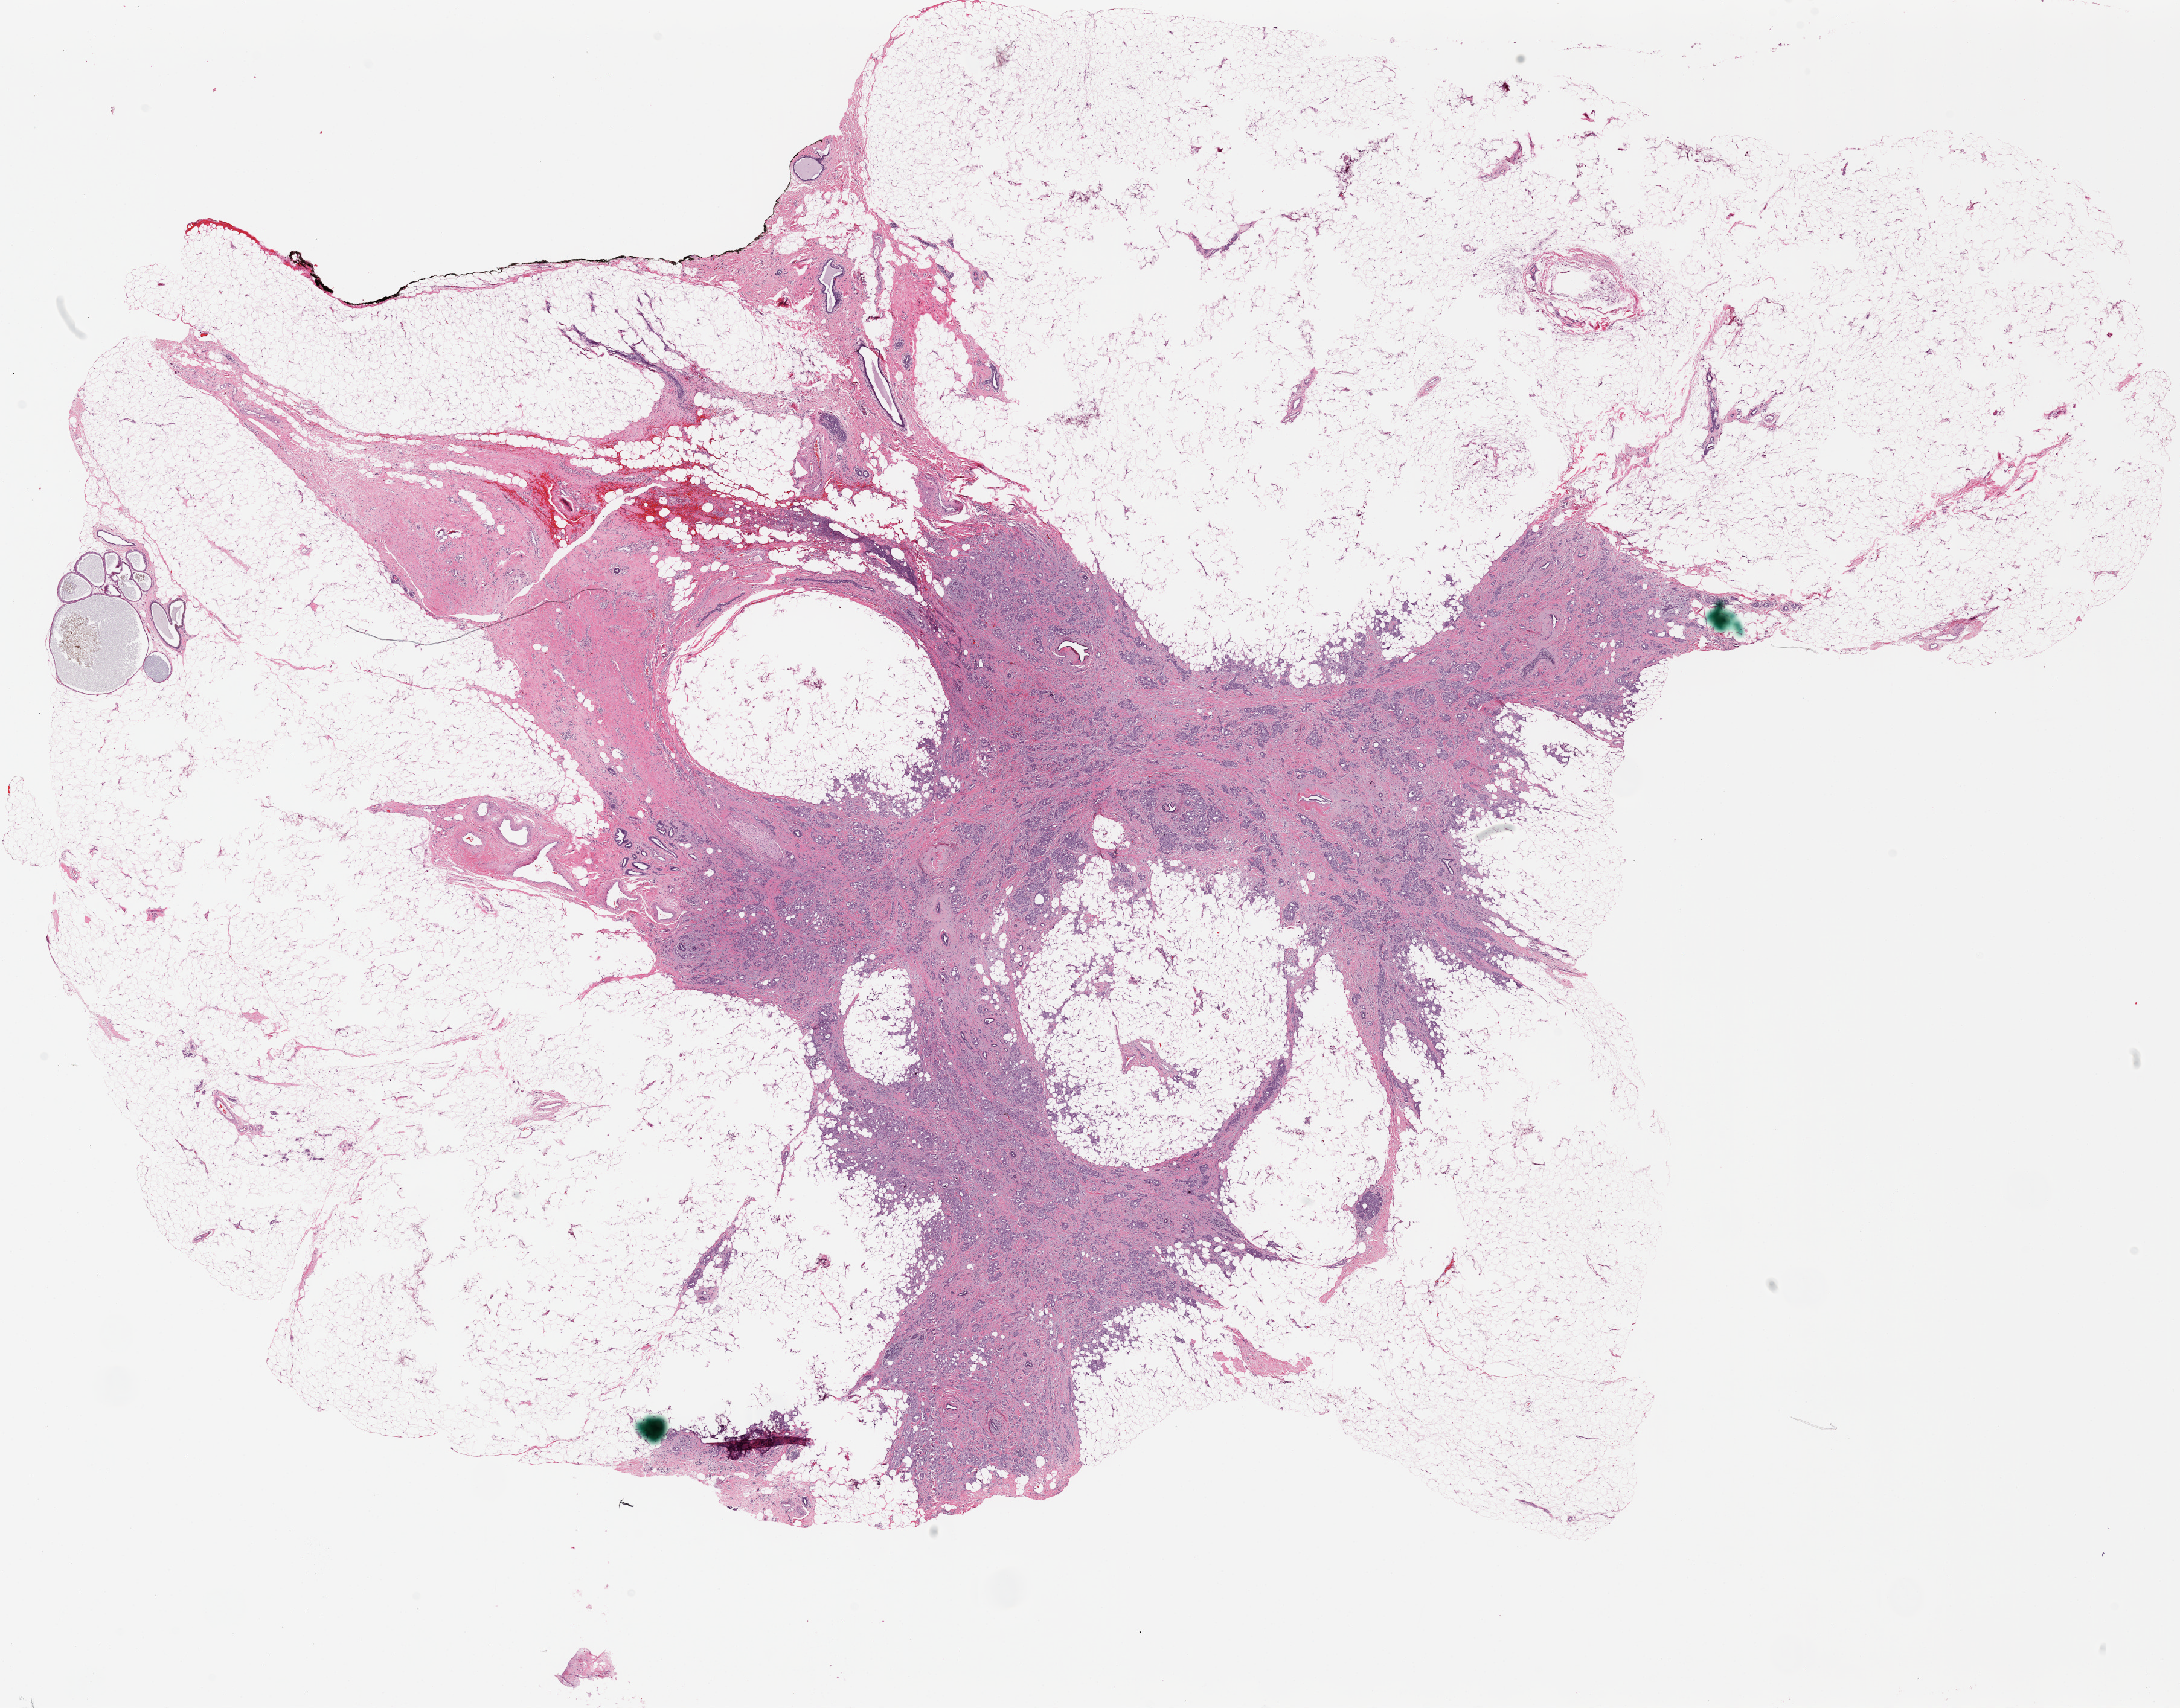
H&E-stained whole-slide image — shown as a low-resolution overview of the whole scanned area (about 28.8 x 22.6 mm, slide scanned at 20x); formalin-fixed paraffin-embedded (FFPE) diagnostic section; breast, primary tumour sample. Female patient; age at initial diagnosis 68 years.
Diagnosis: Infiltrating duct carcinoma, NOS. AJCC pathologic stage: IIA.